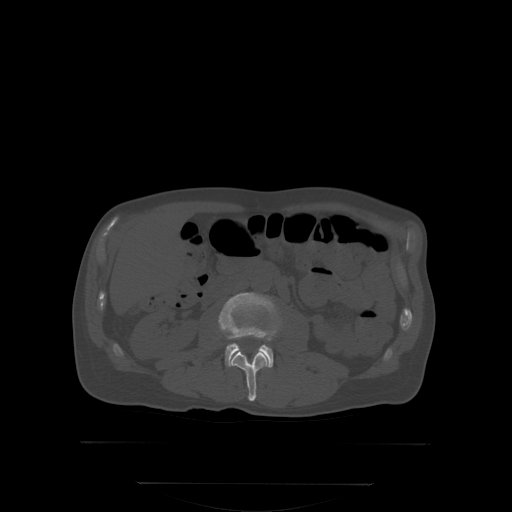
CT including the spine, one axial slice. Bone window (W 1800 / L 400 HU). 2.5 mm slice thickness. 512 × 512 image matrix, field of view 500 × 500 mm. Patient: male, 58 years. From the clinical record (not read from this slice): primary cancer: prostate.
Outlined on this slice (semi-automatic segmentation, software-assisted and operator-edited):
- L2 vertebra: bounding box <231,350,268,401> (left, top, right, bottom; pixels)
- L3 vertebra: <220,294,279,367>